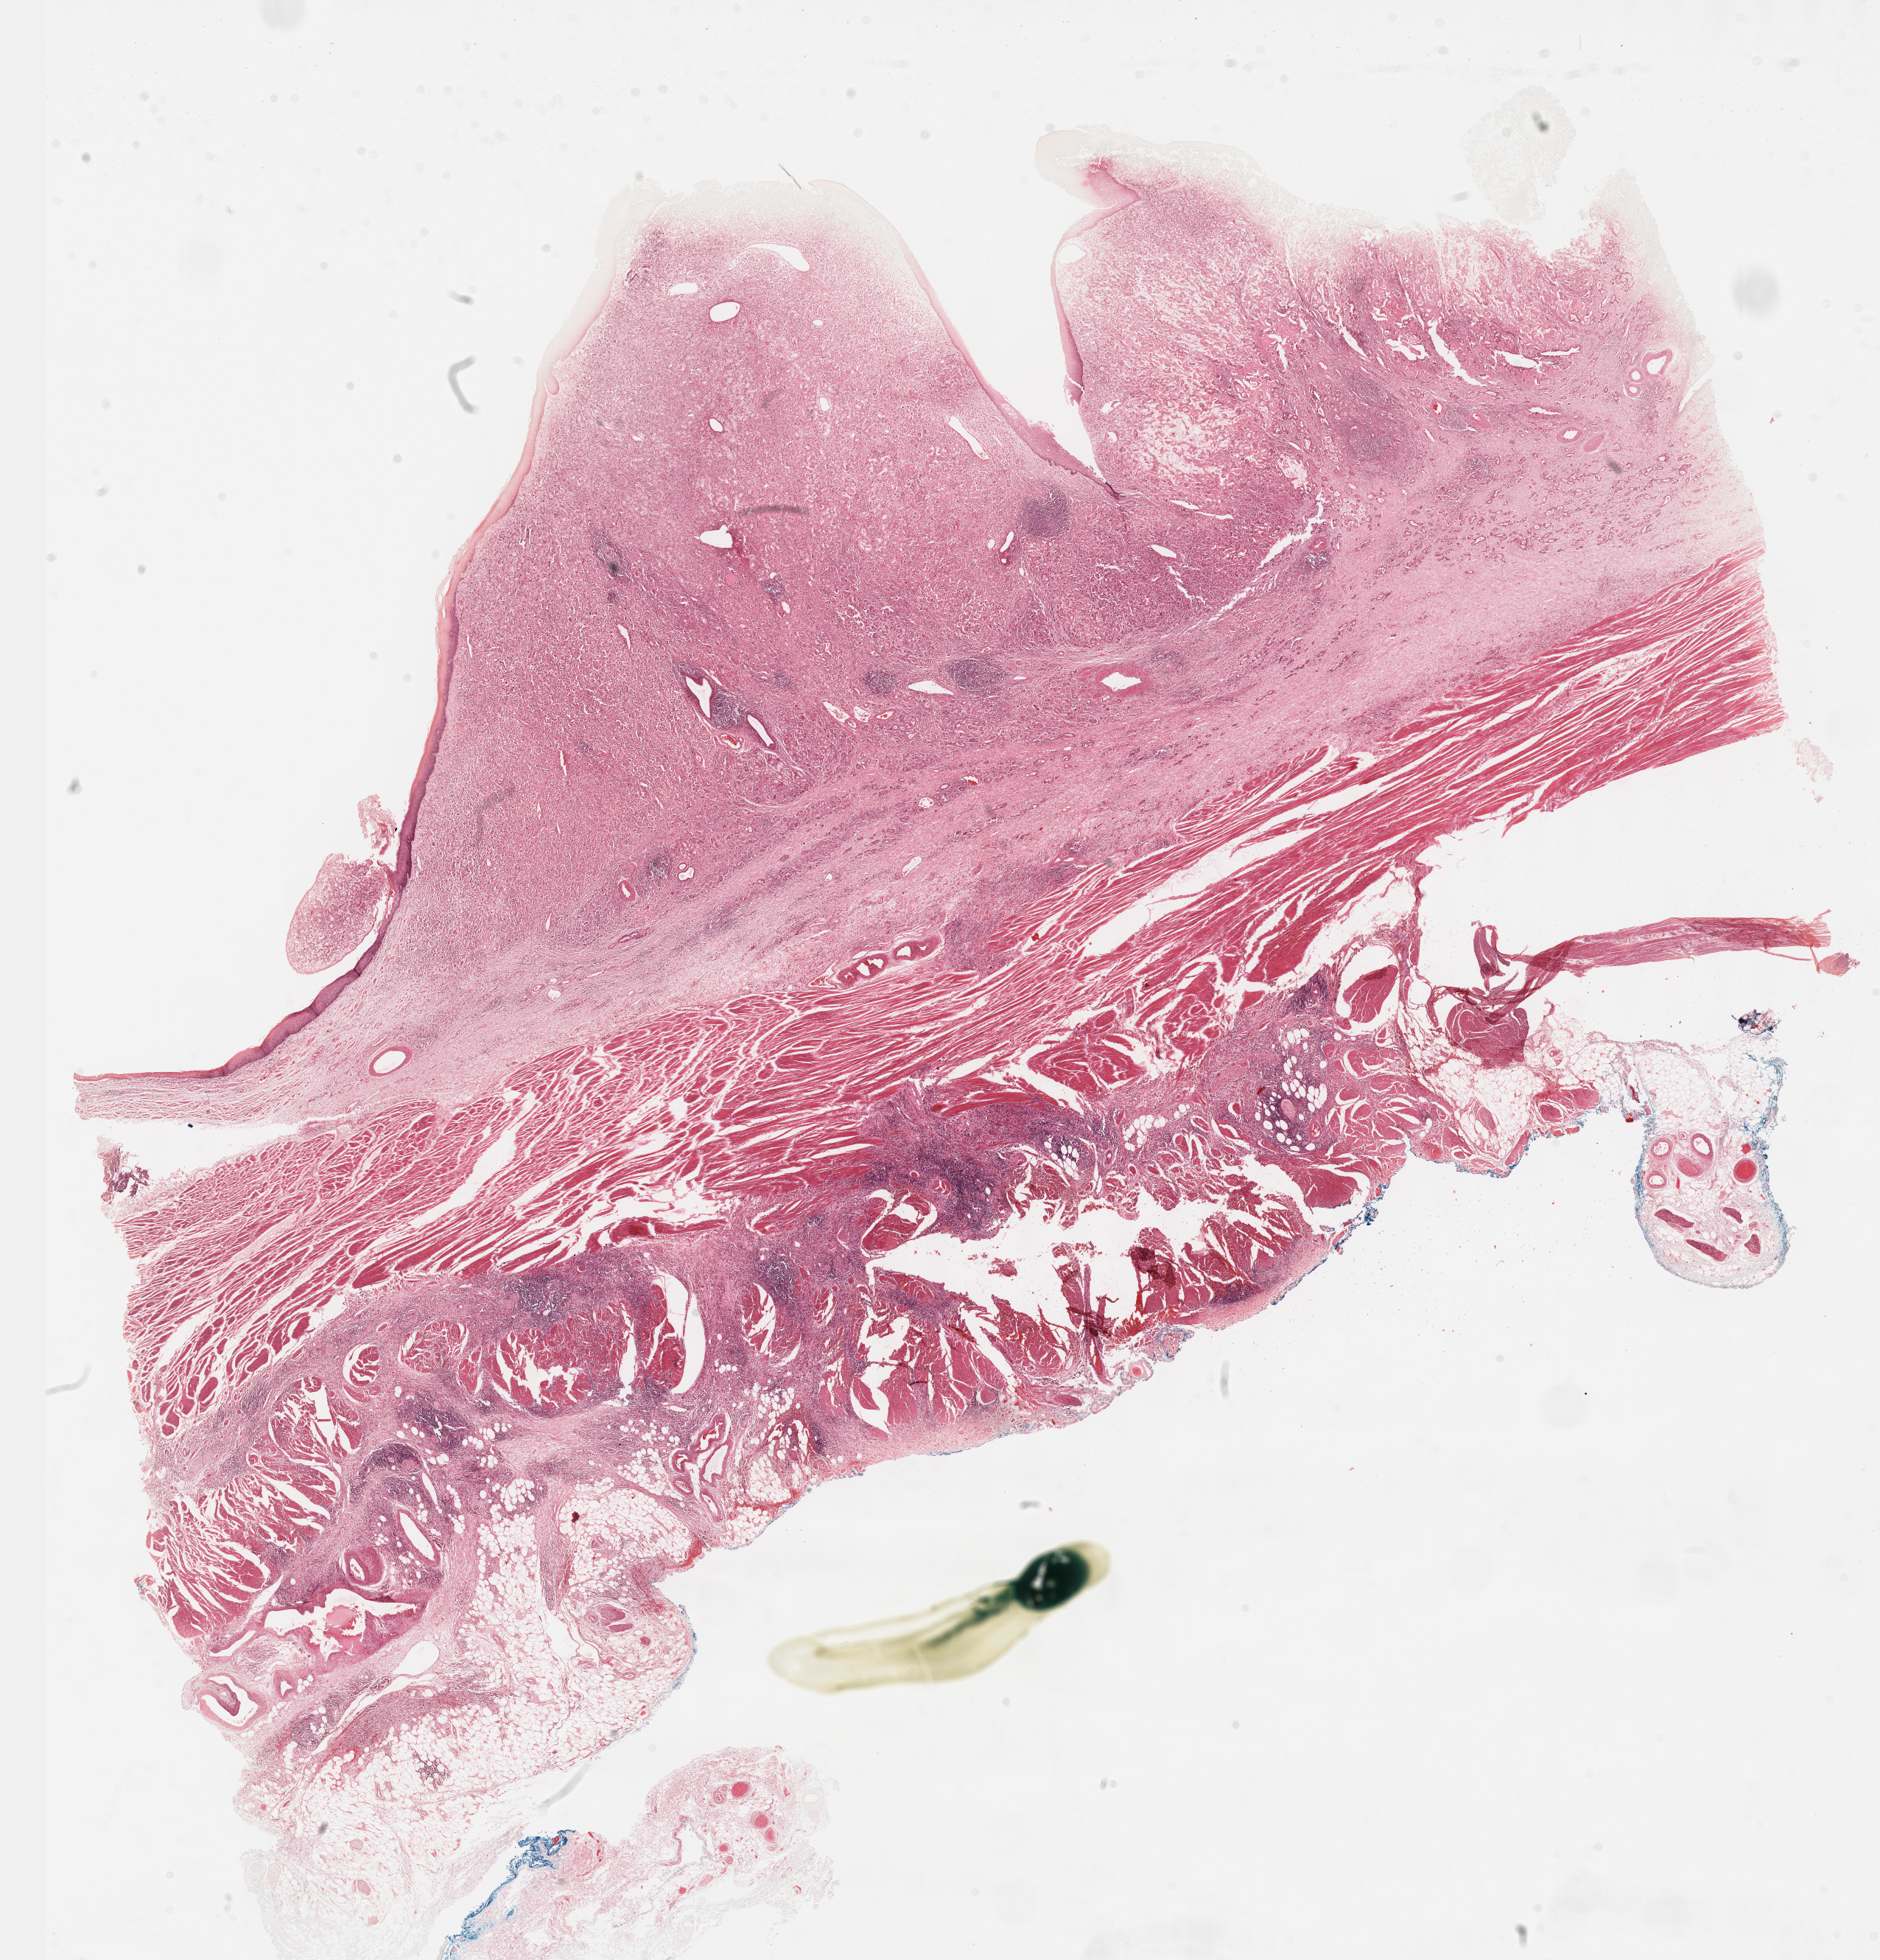
Whole-slide histology image, Hematoxylin and eosin (H&E) stained, a low-resolution overview of the entire scanned area, about 20.6 x 21.5 mm (slide scanned at 40x). Formalin-fixed paraffin-embedded (FFPE) diagnostic section. Sample: primary tumour, esophagus. Male, age 74 years at initial diagnosis. Histologic grade: G3 (poorly differentiated).
Histologic diagnosis: Adenocarcinoma, NOS. Lymph nodes positive (case pathology): 2 of 7 examined. AJCC pathologic stage: III (5th edition). TNM: T3 N1 M0.